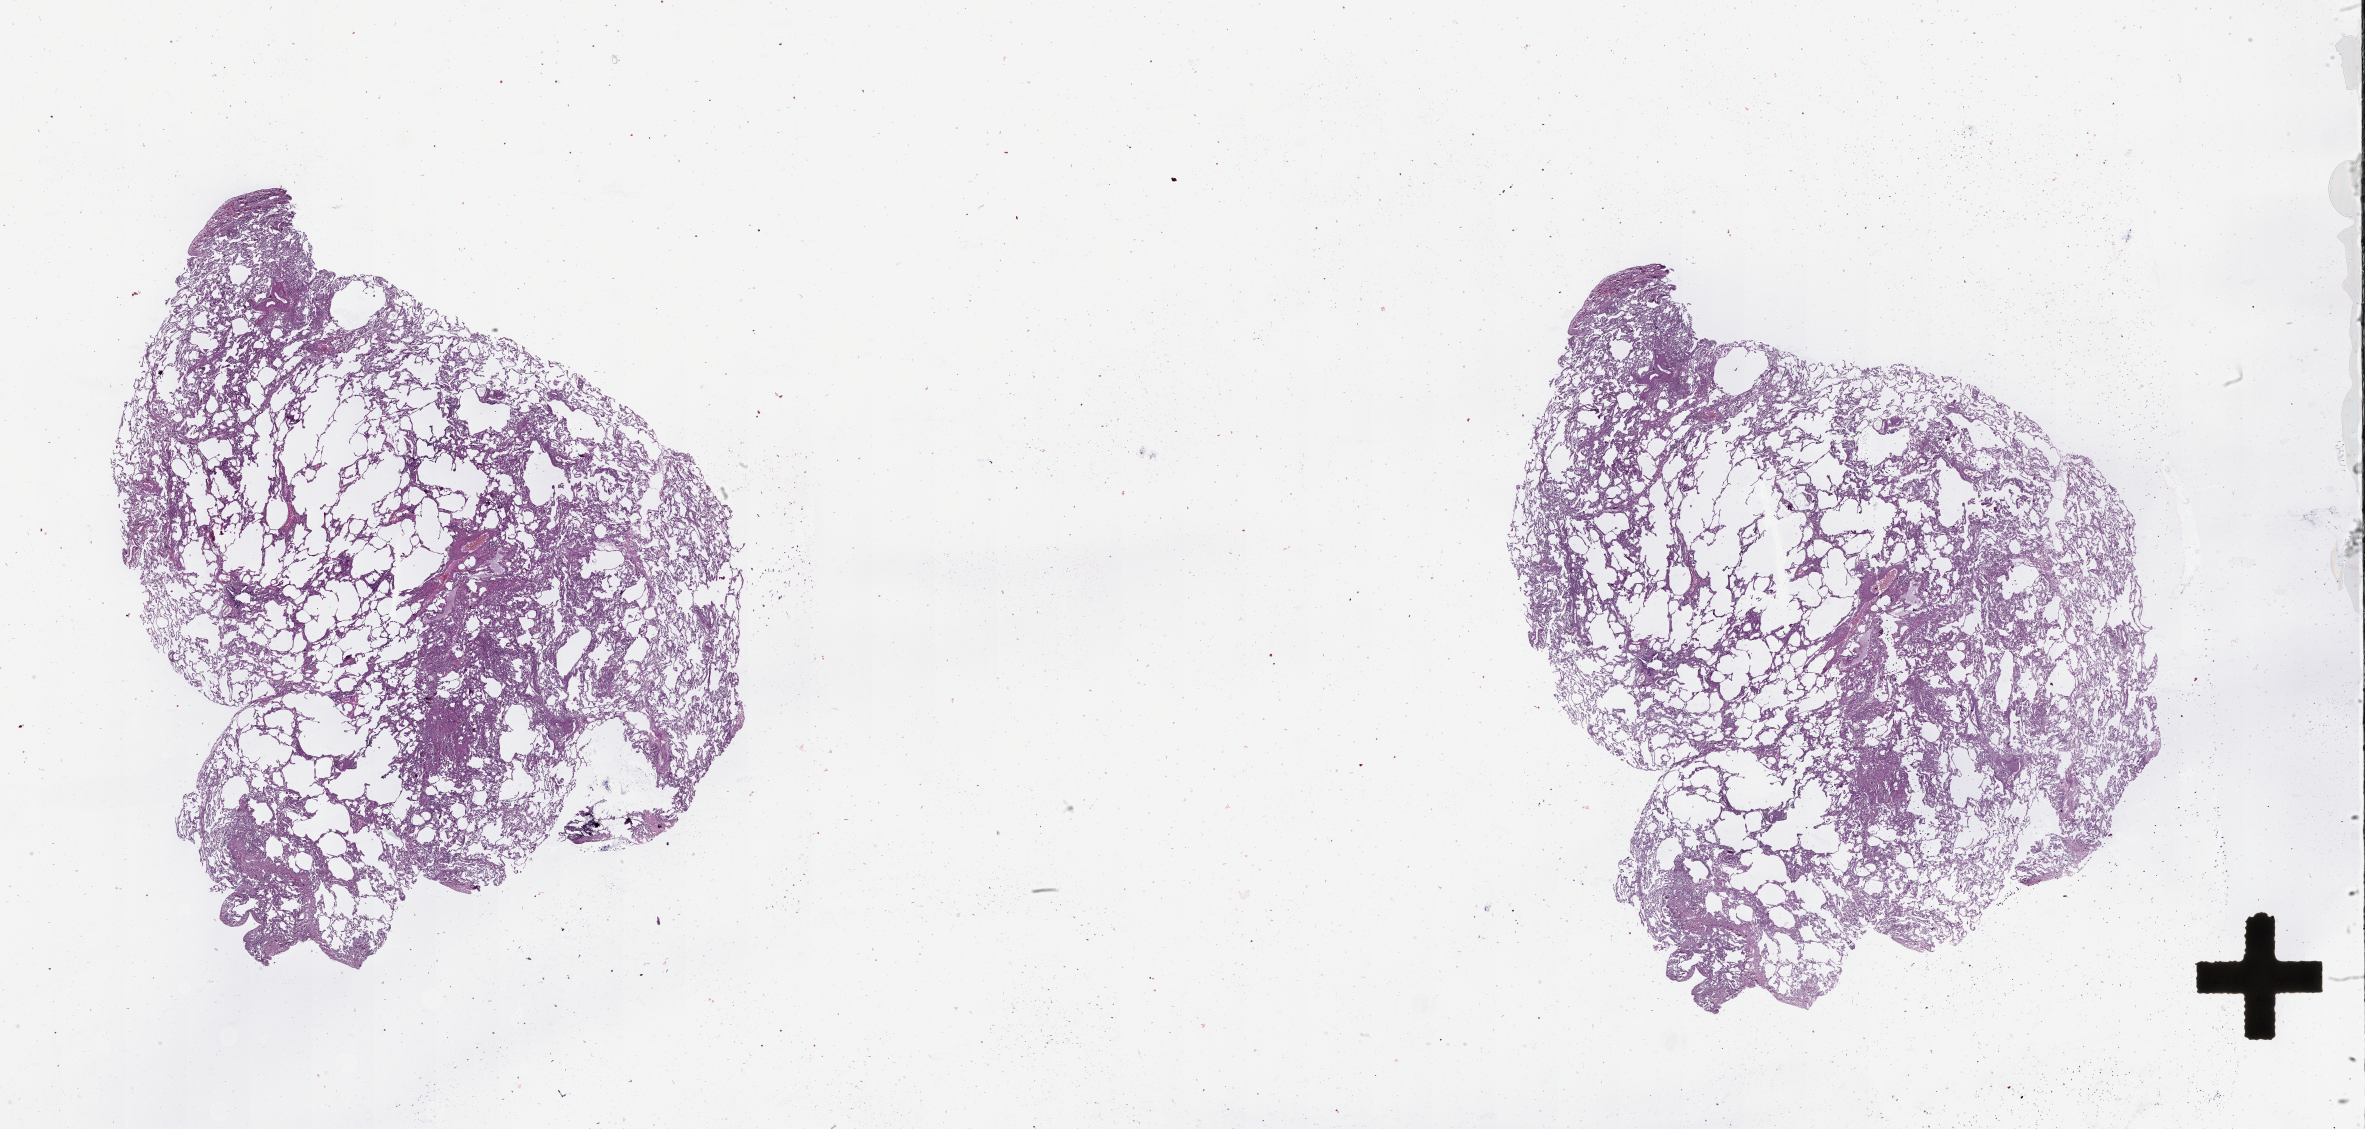
Whole-slide histology image, Hematoxylin and eosin (H&E) stained, whole scanned area (about 38.1 x 18.2 mm, acquisition: 20x scan) shown as a low-resolution overview, lung, tissue type not recorded.
Patient diagnosis (cohort enrolment): lung adenocarcinoma (lung).